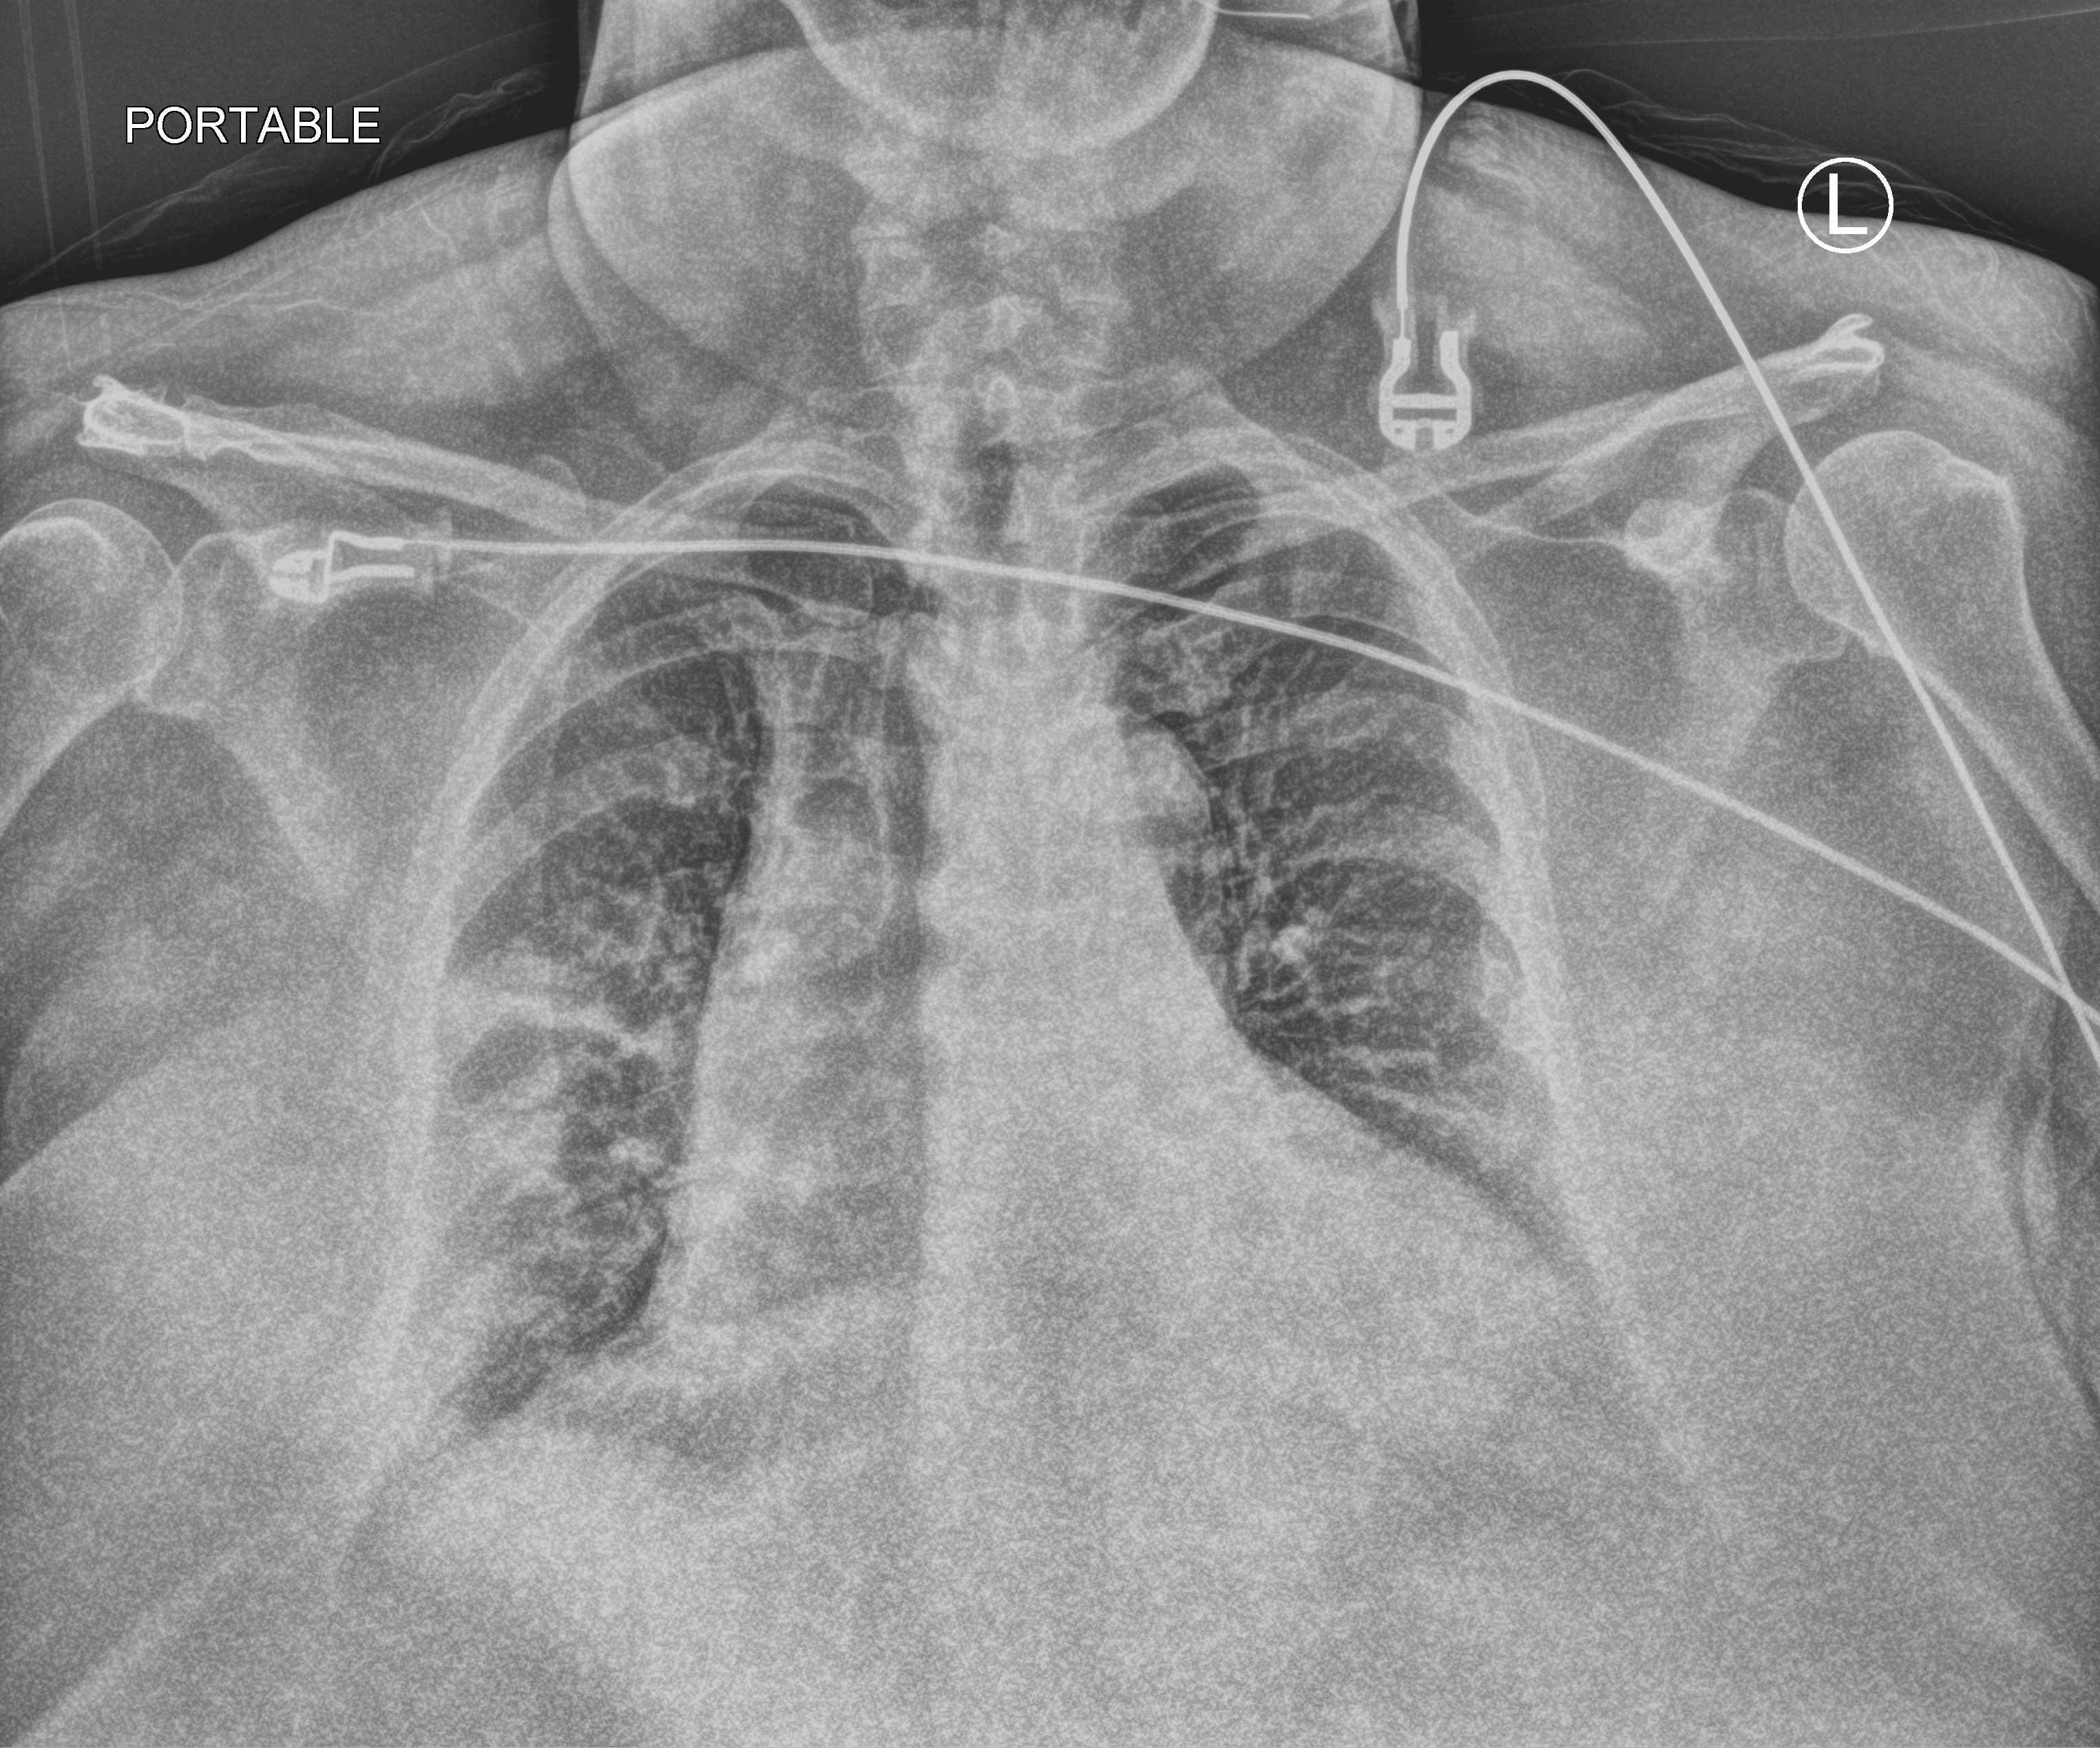
Bedside chest radiograph (computed radiography); anteroposterior (AP) projection. Patient hospitalised with COVID-19; female, aged 60–74 years.
From the hospital-stay record, not from the radiograph (when in the stay this image was taken is not recorded): admitted to intensive care during this hospital stay: no.